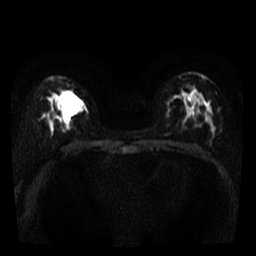
Breast MRI, one axial slice. Diffusion-weighted series; image 2 of 4 stored at this slice position (different b-values; order by instance number). 3 T. 5 mm slice thickness. 256 × 256 image matrix, field of view 280 × 280 mm. Female patient.
Annotated regions visible in this slice (outlined manually by an expert reader):
- tumour on diffusion-weighted imaging: bounding box (x1, y1, x2, y2) in pixels: (64, 92, 81, 113)